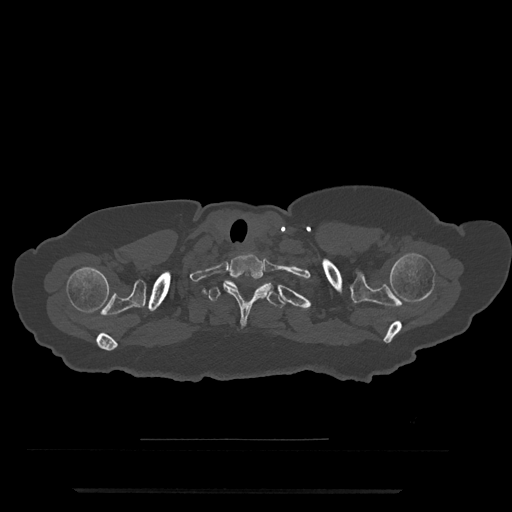
CT including the spine, one axial slice. Slice 698 of 797 in the series (ordered by position). 120 kVp. Bone window (W 1800 / L 400 HU). 512 × 512 image matrix, field of view 440 × 440 mm. Female patient, age 51 years. Case-level facts recorded for this patient, not image findings: primary cancer: neuro; vertebrae with lytic lesions (as recorded): T8.
Annotated regions visible in this slice (semi-automatic segmentation, software-assisted and operator-edited):
- T1 vertebra: box from (x=223, y=253) to (x=272, y=326) px
- T2 vertebra: (x=209, y=280)–(x=286, y=309)